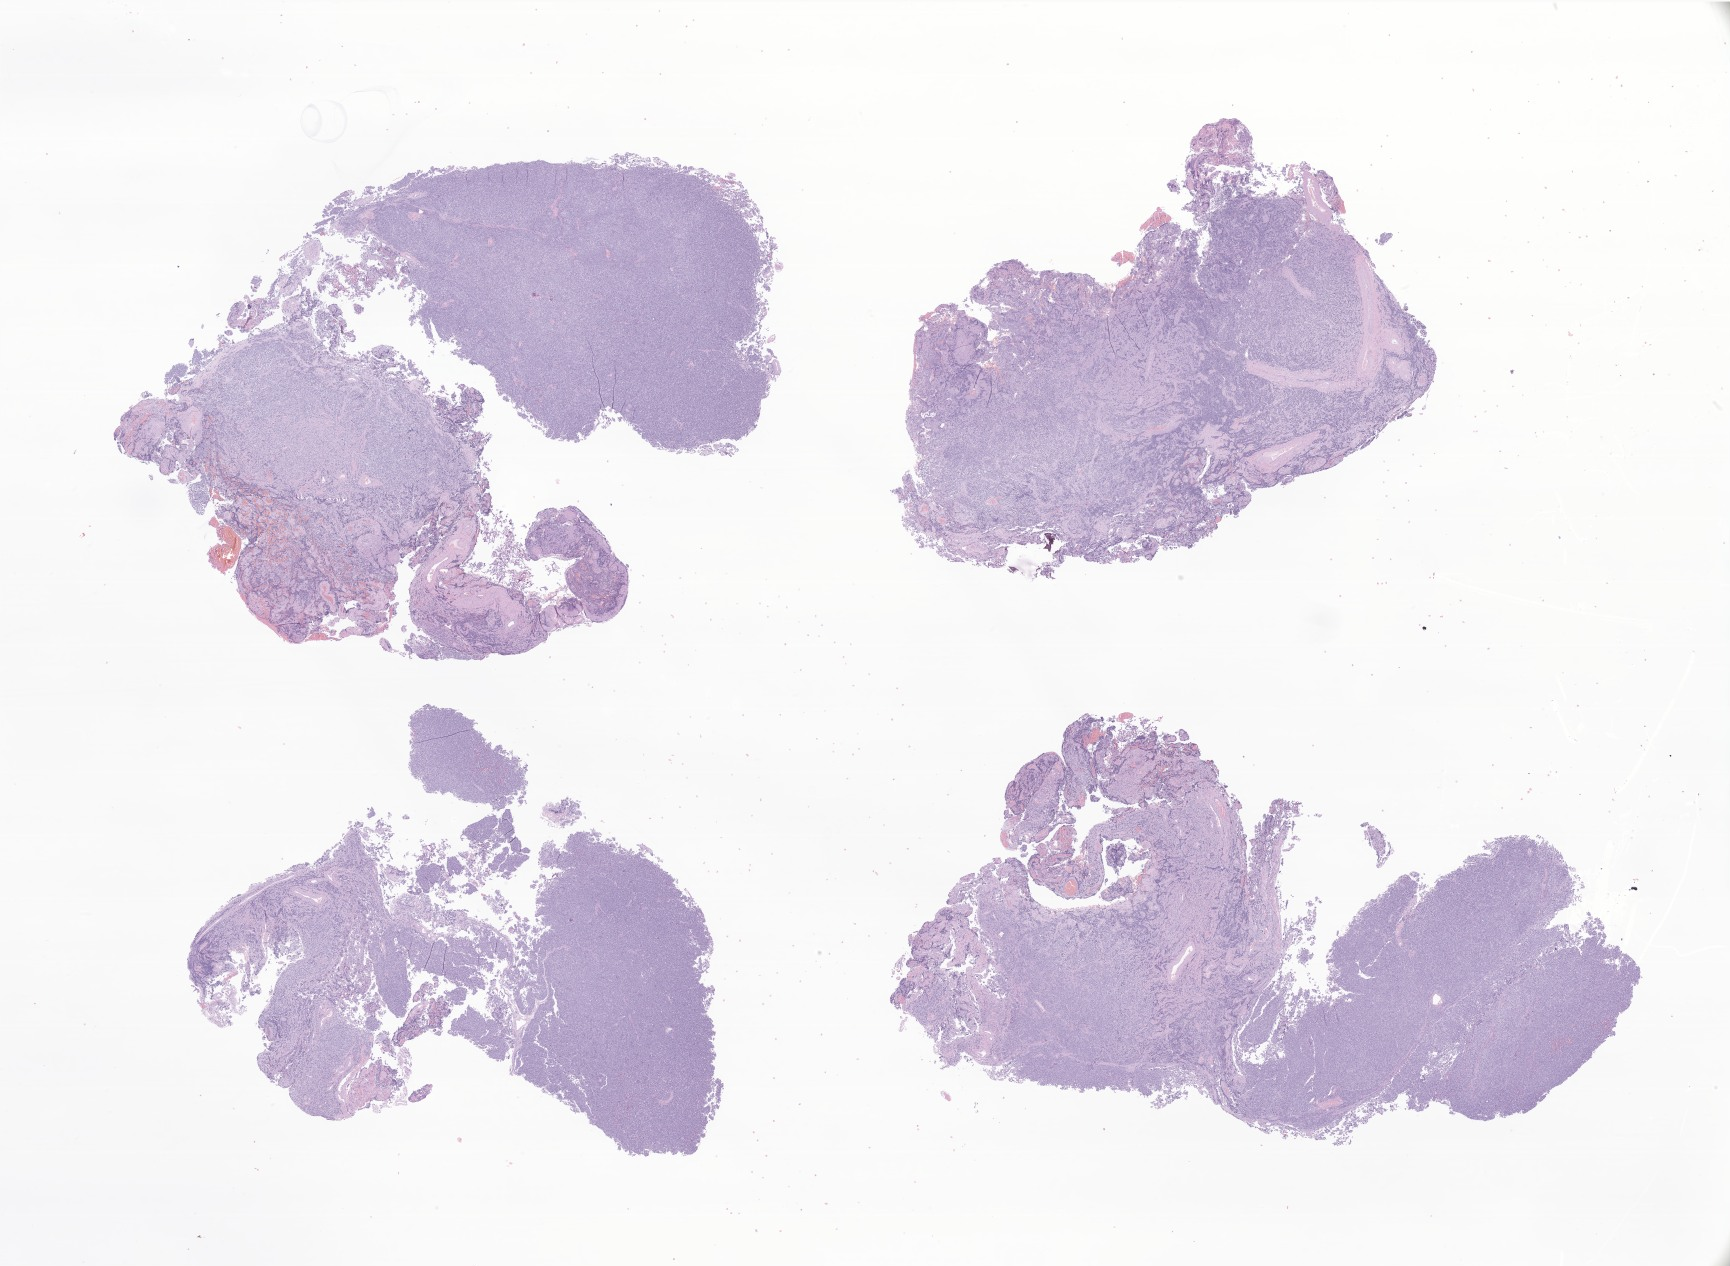
Digitized H&E-stained section of tumor tissue from the brain — a low-resolution overview of the entire scanned area, about 29.2 x 21.4 mm, FFPE section. Patient male; age 107 months (8 years 11 months).
• diagnosis: Medulloblastoma, NOS